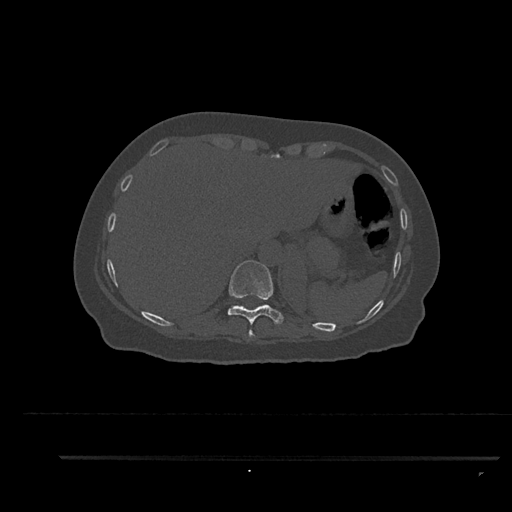
CT including the spine, one axial slice; slice 363 of 797 in the series (ordered by position); bone window (W 1800 / L 400 HU); 512 × 512 image matrix. Patient: female, 44 years. Case-level facts recorded for this patient, not image findings: primary cancer: renal; vertebrae with lytic lesions (as recorded): L1.
Structures marked on this image (semi-automatic segmentation, software-assisted and operator-edited):
- T10 vertebra: box from (x=227, y=260) to (x=284, y=330) px
- T9 vertebra: (x=249, y=330)–(x=255, y=337)